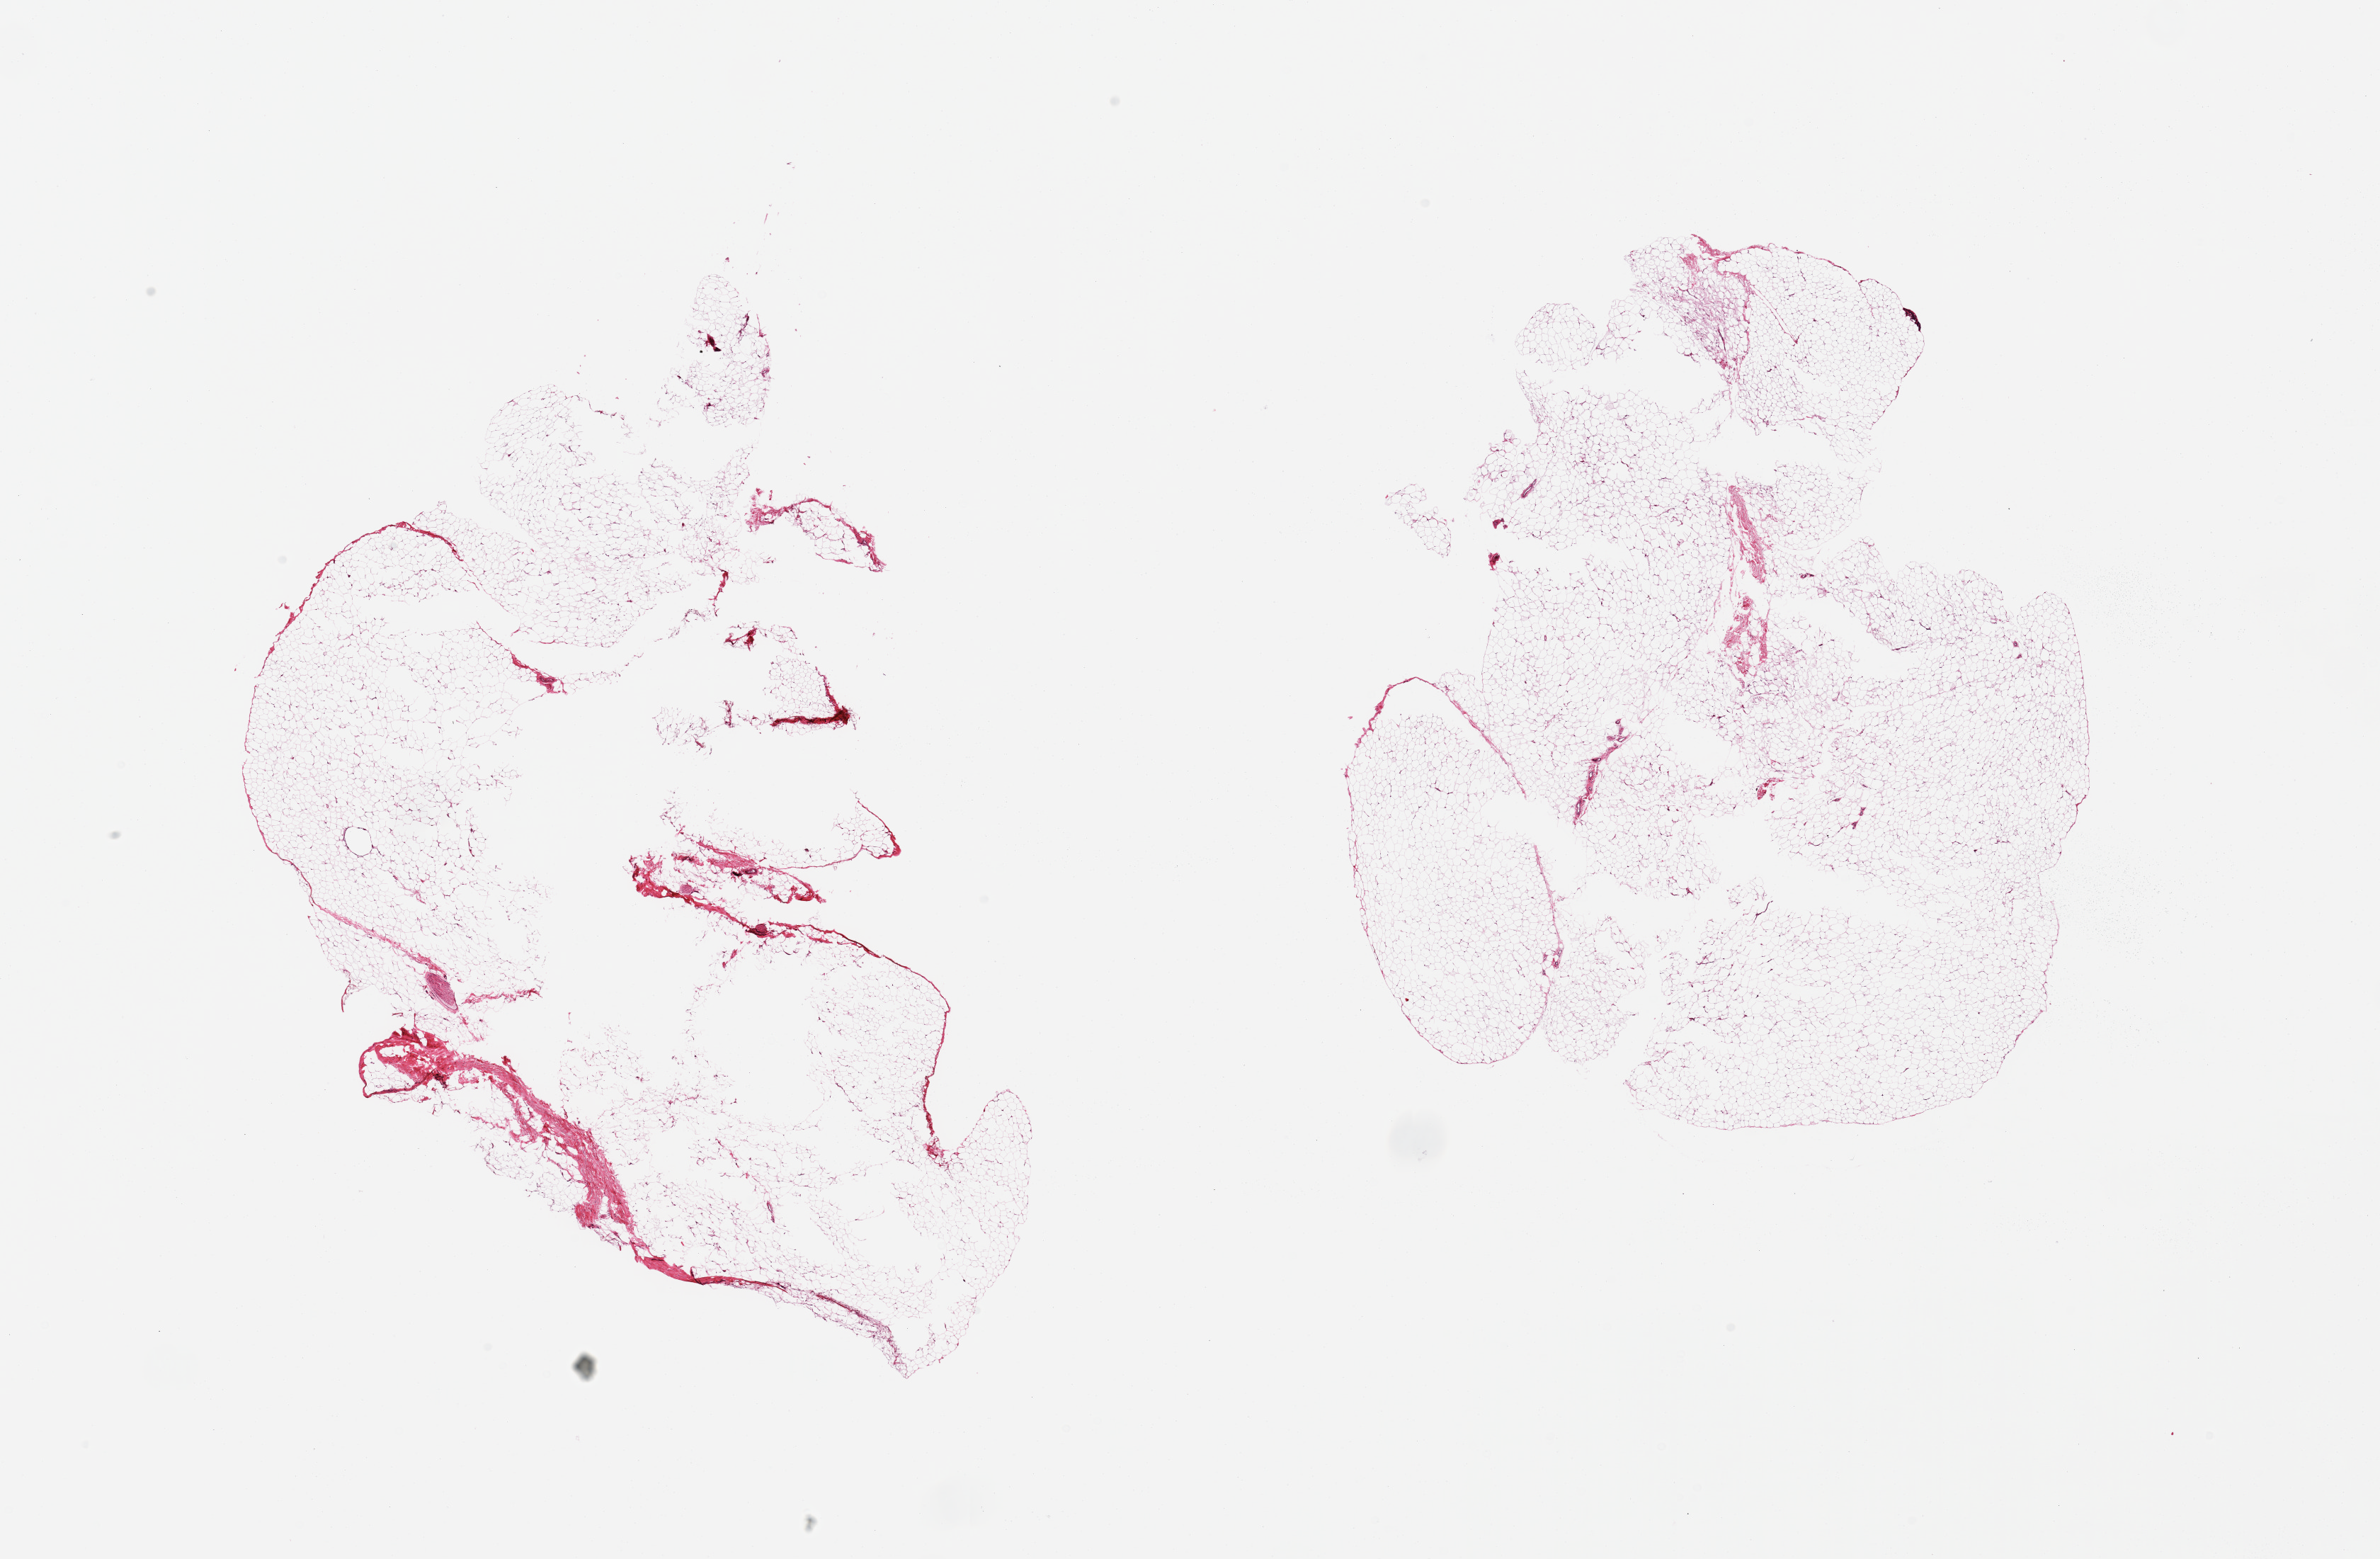
Digitized H&E-stained section, a low-resolution overview of the entire scanned area, about 26.6 x 17.4 mm (from a 20x scan); PAXgene-fixed, paraffin-embedded tissue; section of breast (target tissue); donor tissue sample. Donor: male.
Pathologist's review note for this sample: 2 pieces, fibroadipose elements only.